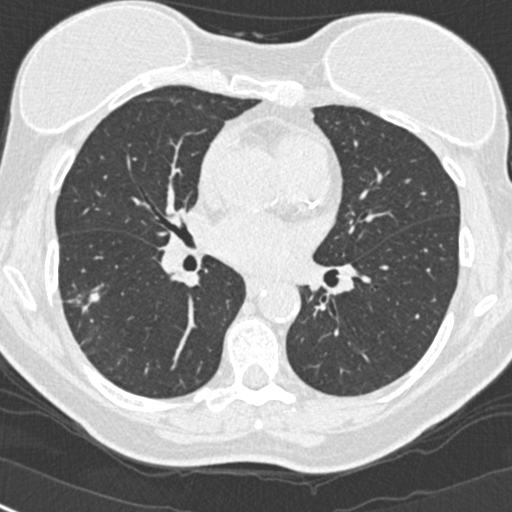
Low-dose screening chest CT, one axial slice. 120 kVp. Lung window (W 1500 / L -600 HU). 512 × 512 image matrix, field of view 296 × 296 mm.
Structures marked on this image (outlined manually by an expert reader):
- lesion 1 (tumor, upper lobe of right lung): bounding box (x1, y1, x2, y2) in pixels: (71, 292, 100, 313)